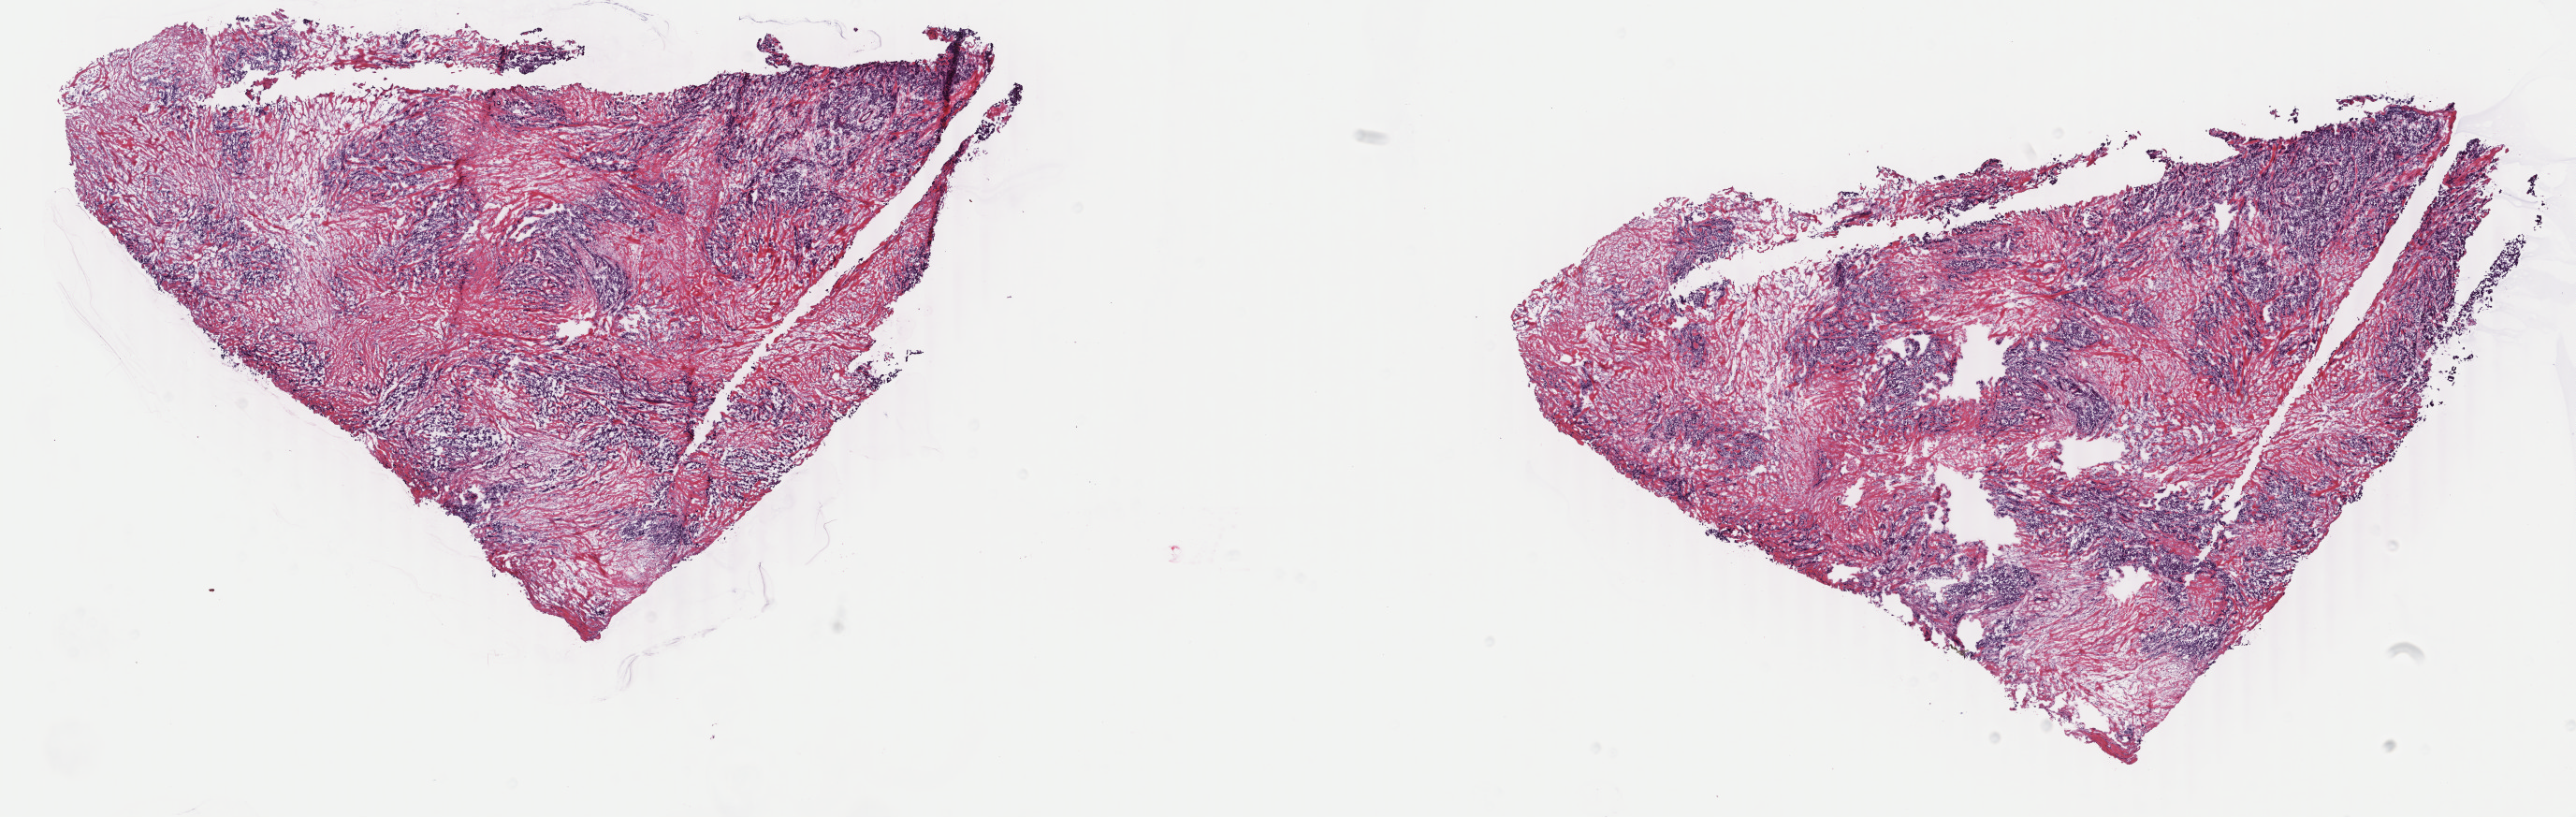
Whole-slide histology image, Hematoxylin and eosin (H&E) stained, whole scanned area (about 21.9 x 6.9 mm, from a 40x scan) shown as a low-resolution overview; frozen section; primary tumour sample from the breast. Female, age 58 years at initial diagnosis. Slide review estimates, as recorded: tumour cells 50%, tumour nuclei 70%, normal cells 0%, stromal cells 50%, necrosis 0%. Inflammatory infiltration, as recorded: lymphocyte infiltration 0%, monocyte infiltration 0%, neutrophil infiltration 0%.
AJCC pathologic stage: IIA (7th edition). Lymph nodes positive (case pathology): 0 of 12 examined. Diagnosis: Infiltrating duct carcinoma, NOS.